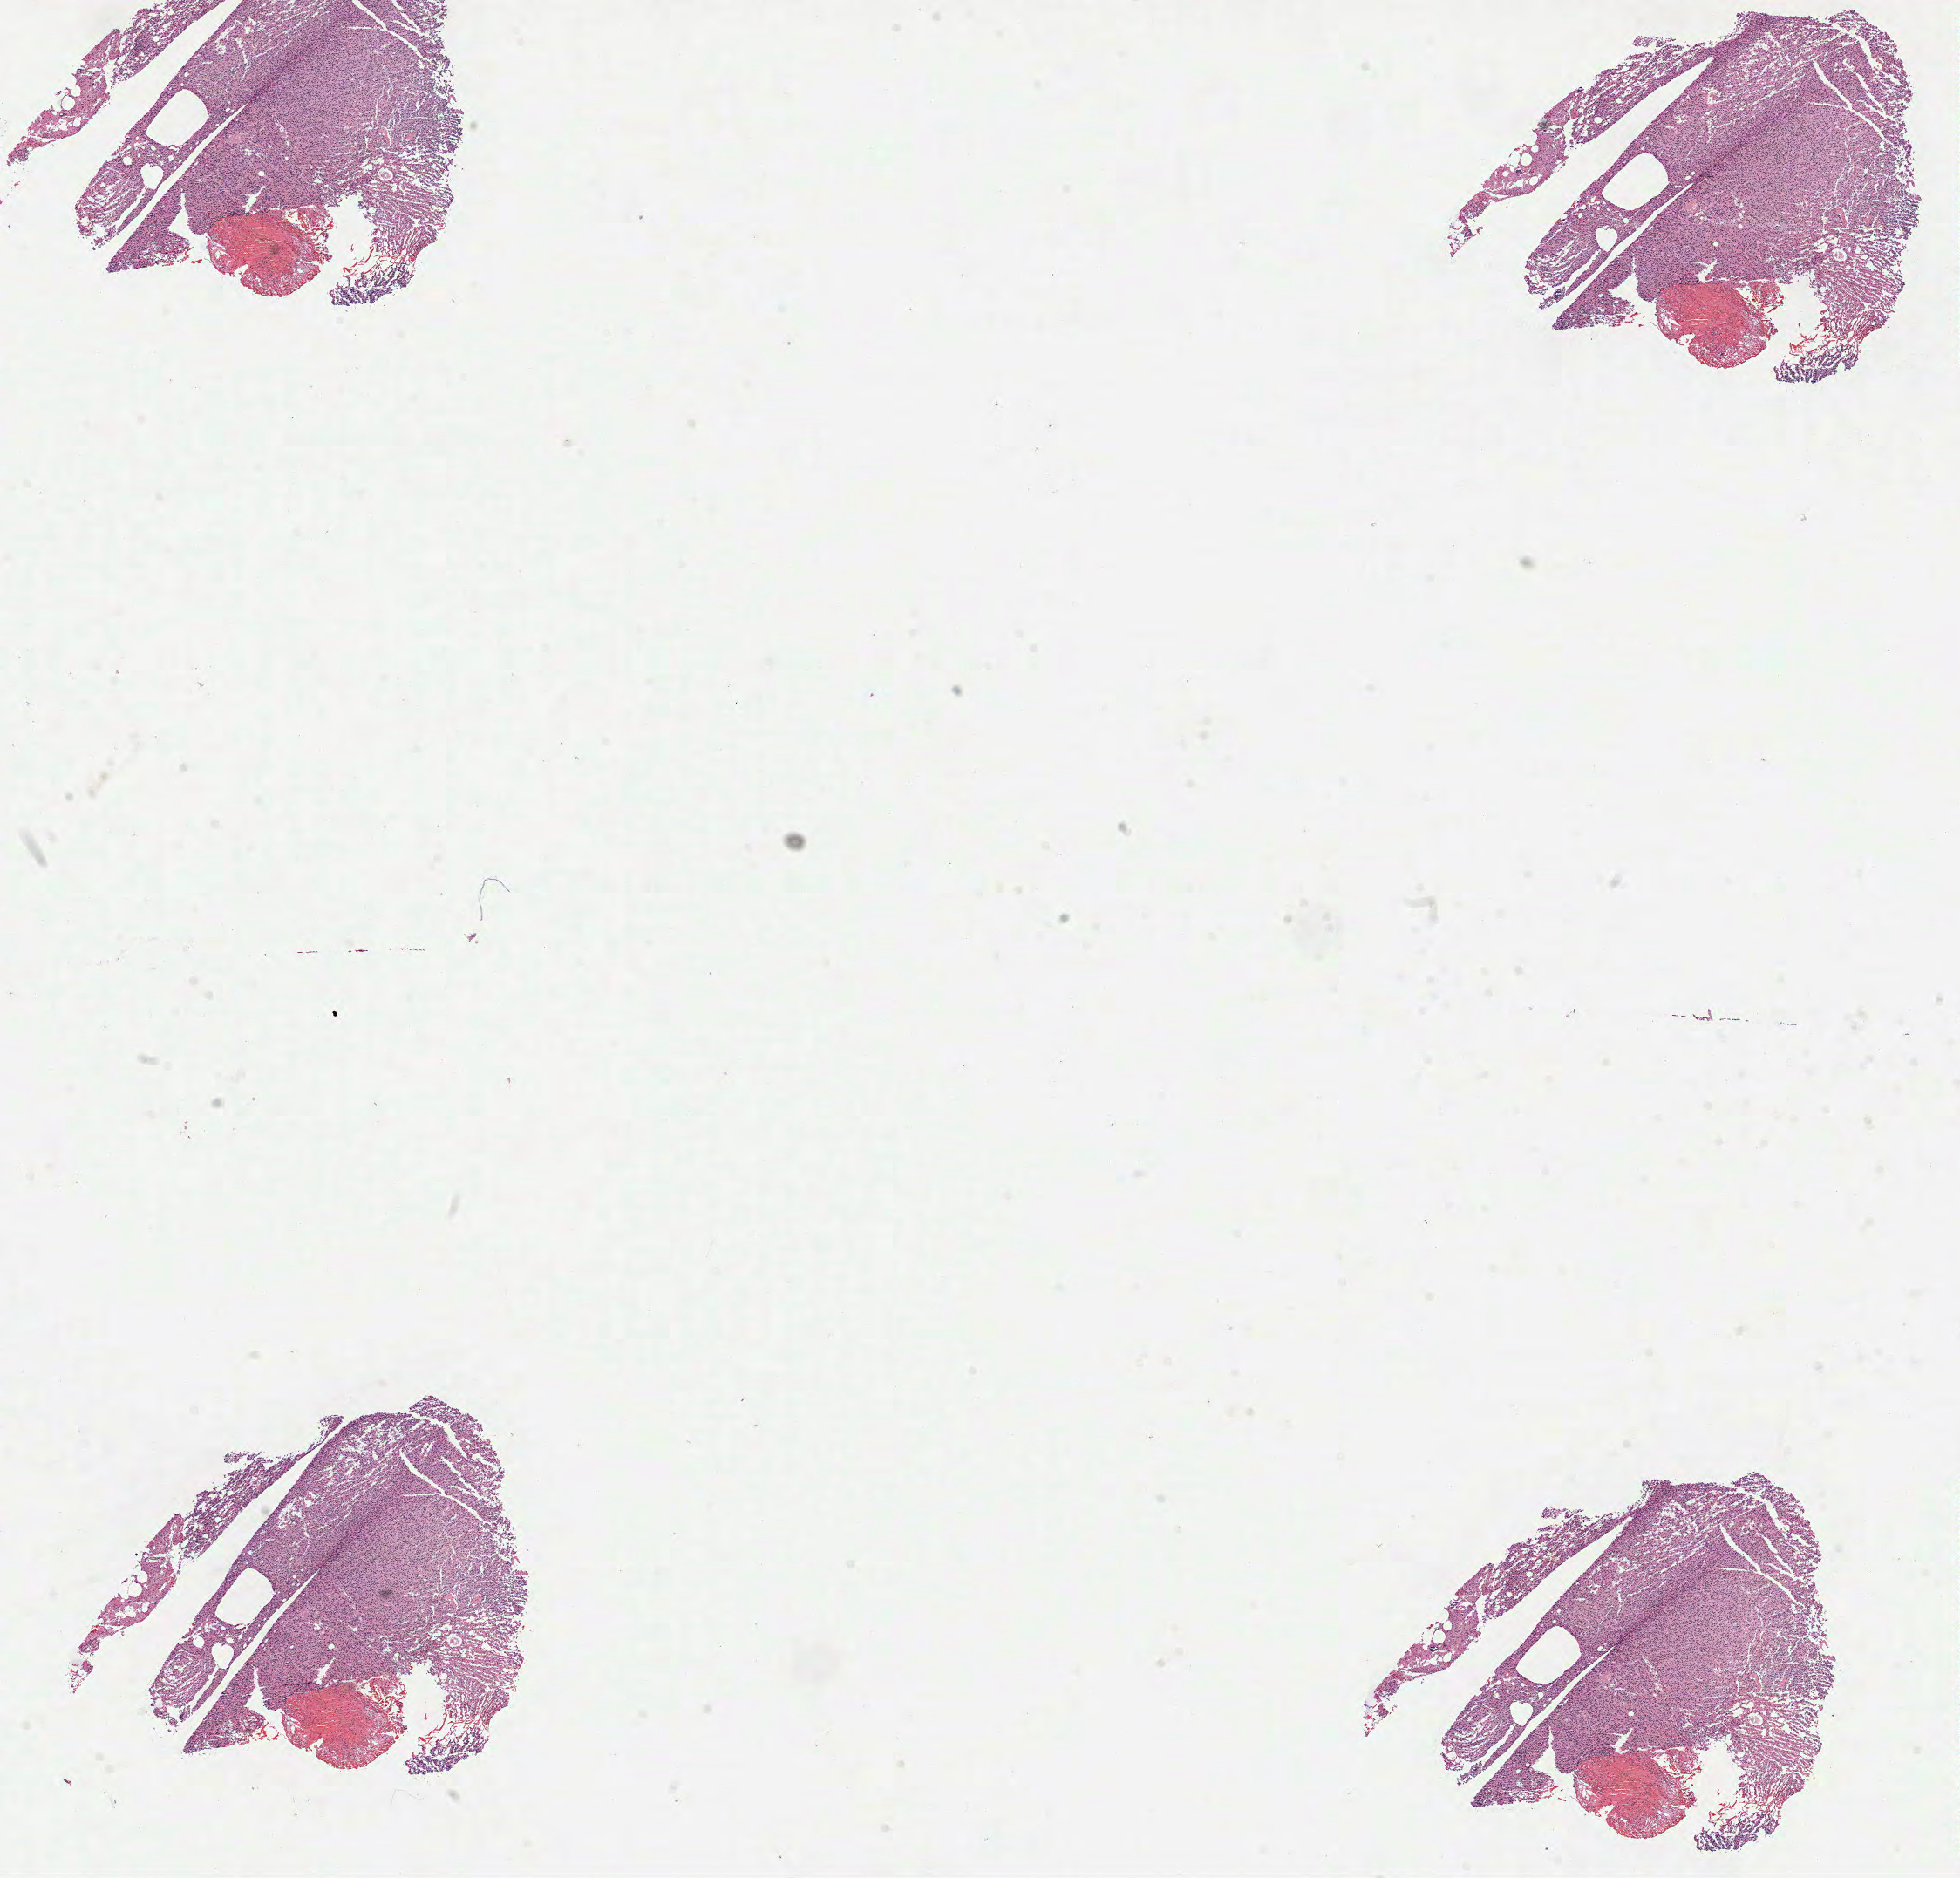
Whole-slide histology image, H&E, a low-resolution overview of the entire scanned area, about 18.1 x 17.4 mm (acquisition: 40x scan), FFPE section, brain, primary tumour sample. Patient: female, age at initial diagnosis 66 years. Histologic grade: G2 (moderately differentiated).
Laterality: left. Diagnosis: Oligodendroglioma, NOS (cerebrum).